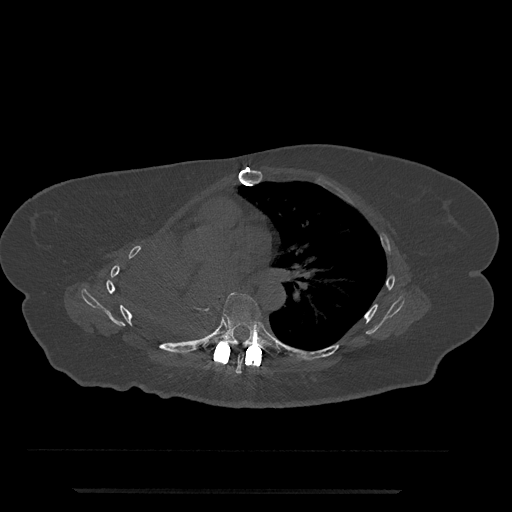
CT including the spine, one axial slice. Slice 460 of 797 in the series (ordered by position). Reconstruction kernel Br40s/3. Bone window (W 1800 / L 400 HU). 0.5 mm slice thickness. 512 × 512 image matrix, field of view 440 × 440 mm. Female patient, age 51 years. From the clinical record (not read from this slice): primary cancer: neuro; vertebrae with lytic lesions (as recorded): T8.
Annotated regions visible in this slice (semi-automatically segmented with operator editing):
- T6 vertebra: bounding box <236,354,244,373> (left, top, right, bottom; pixels)
- T7 vertebra: <204,293,279,357>